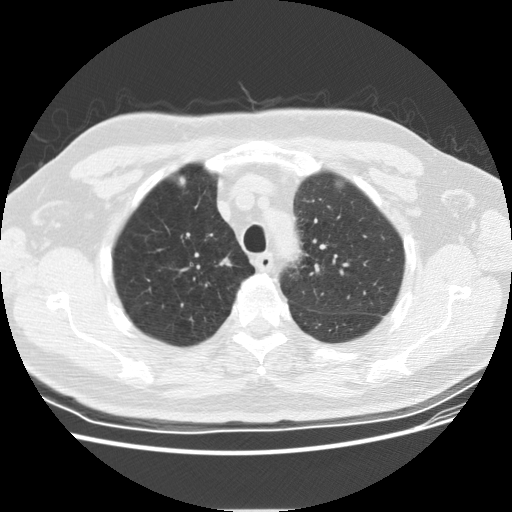
Axial slice from a low-dose chest CT screening exam; second screening round (one year after baseline); lung window (W 1500 / L -600 HU); 2.5 mm slice thickness; standard (soft-tissue) reconstruction kernel (STANDARD); slice 117 of 152 in the series. Male, age 69 years at enrolment. Current smoker at enrolment.
• Lesion marked by an expert reader, bounding box [x1, y1, x2, y2] px = [209, 248, 242, 279].
• Reader record for this screening exam (exam-level; its link to the box is not recorded): non-calcified nodule or mass ≥4 mm, right lower lobe, 4 × 4 mm, smooth margins, soft tissue attenuation, pre-existing on the prior screen: yes; interval growth: no.
• Lung cancer was diagnosed 435 days after this screen (after the third annual screen): squamous cell carcinoma, NOS, right upper lobe, moderately differentiated (G2), stage IA (AJCC 6th edition), 9 mm at pathology.